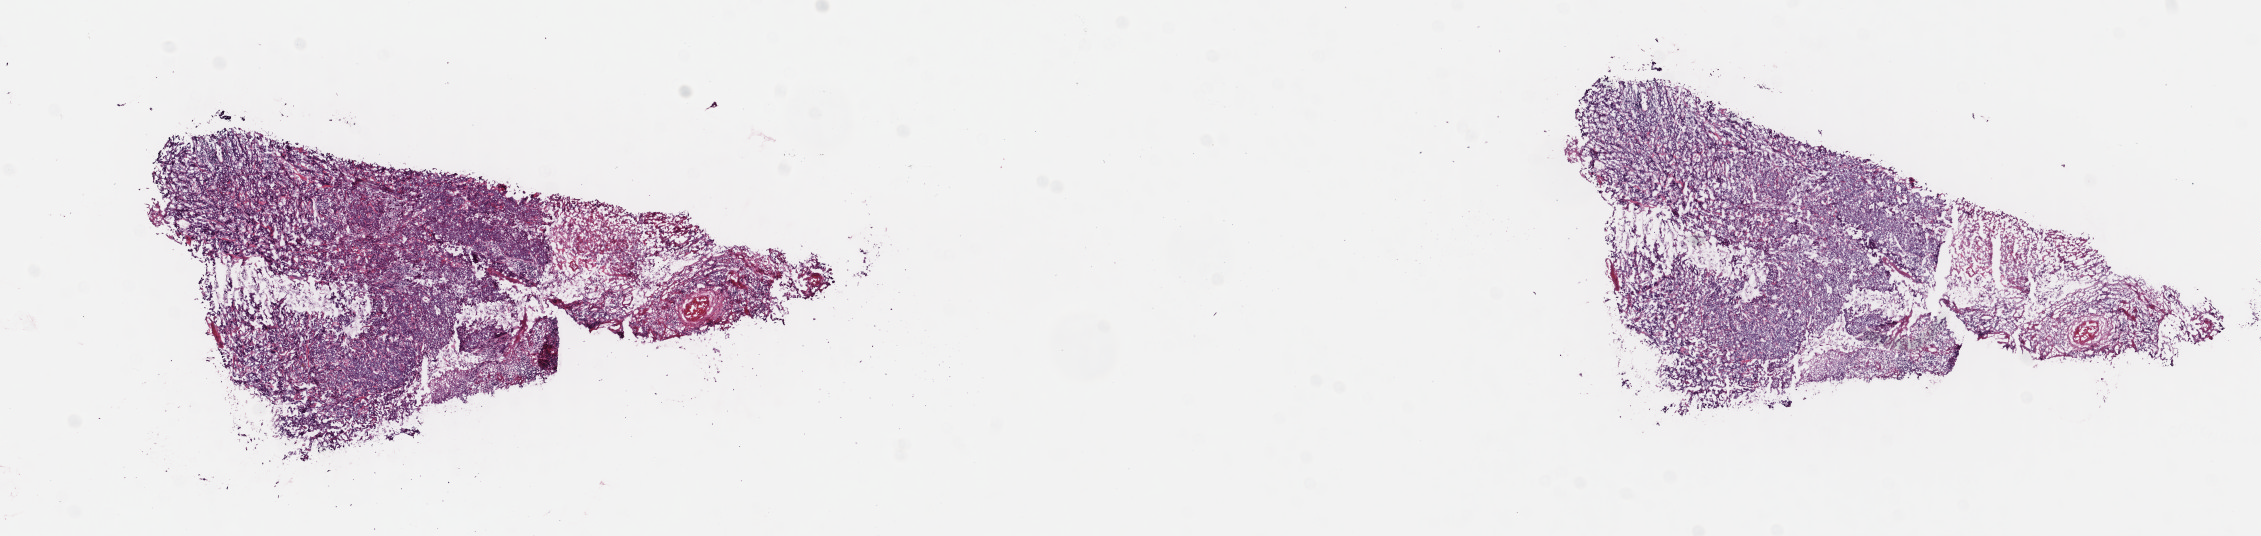
Whole-slide histology image, H&E, a low-resolution overview of the entire scanned area, about 17.8 x 4.2 mm (from a 40x scan); frozen section from the top of the tissue portion; sample: primary tumour, cervix. Patient: female, age at initial diagnosis 38 years. Histologic grade: G3 (poorly differentiated). Composition of this section per pathologist review: tumour cells 75%, tumour nuclei 65%, normal cells 0%, stromal cells 25%, necrosis 0%. Inflammatory infiltration, as recorded: lymphocyte infiltration 0%, monocyte infiltration 0%, neutrophil infiltration 0%.
• FIGO stage: IB
• histologic diagnosis: Squamous cell carcinoma, keratinizing, NOS
• lymph nodes positive (case pathology): 0 of 31 examined